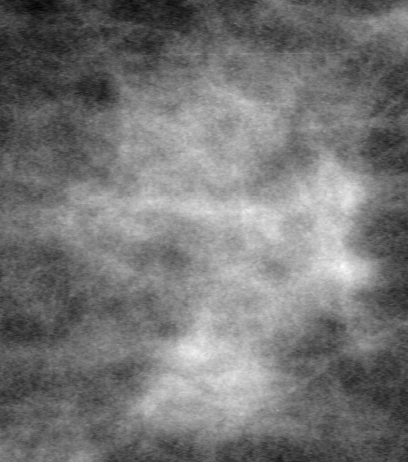
Region of interest cut from a scanned film mammogram (one marked finding), right breast, CC view, BI-RADS breast density category 2 (scale 1–4).
- Mass, shape irregular, margins ill defined; BI-RADS assessment category 4; pathology (as recorded): malignant.